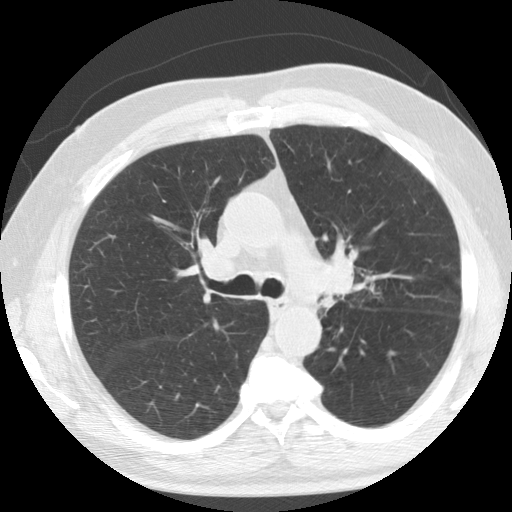
Low-dose screening chest CT, one axial slice; position 86 of 133 along the scan axis; 120 kVp; lung window (W 1500 / L -600 HU); 512 × 512 image matrix.
Structures marked on this image (outlined manually by an expert reader):
- lesion 1 (tumor, upper lobe of left lung): bounding box (x1, y1, x2, y2) in pixels: (319, 253, 353, 310)